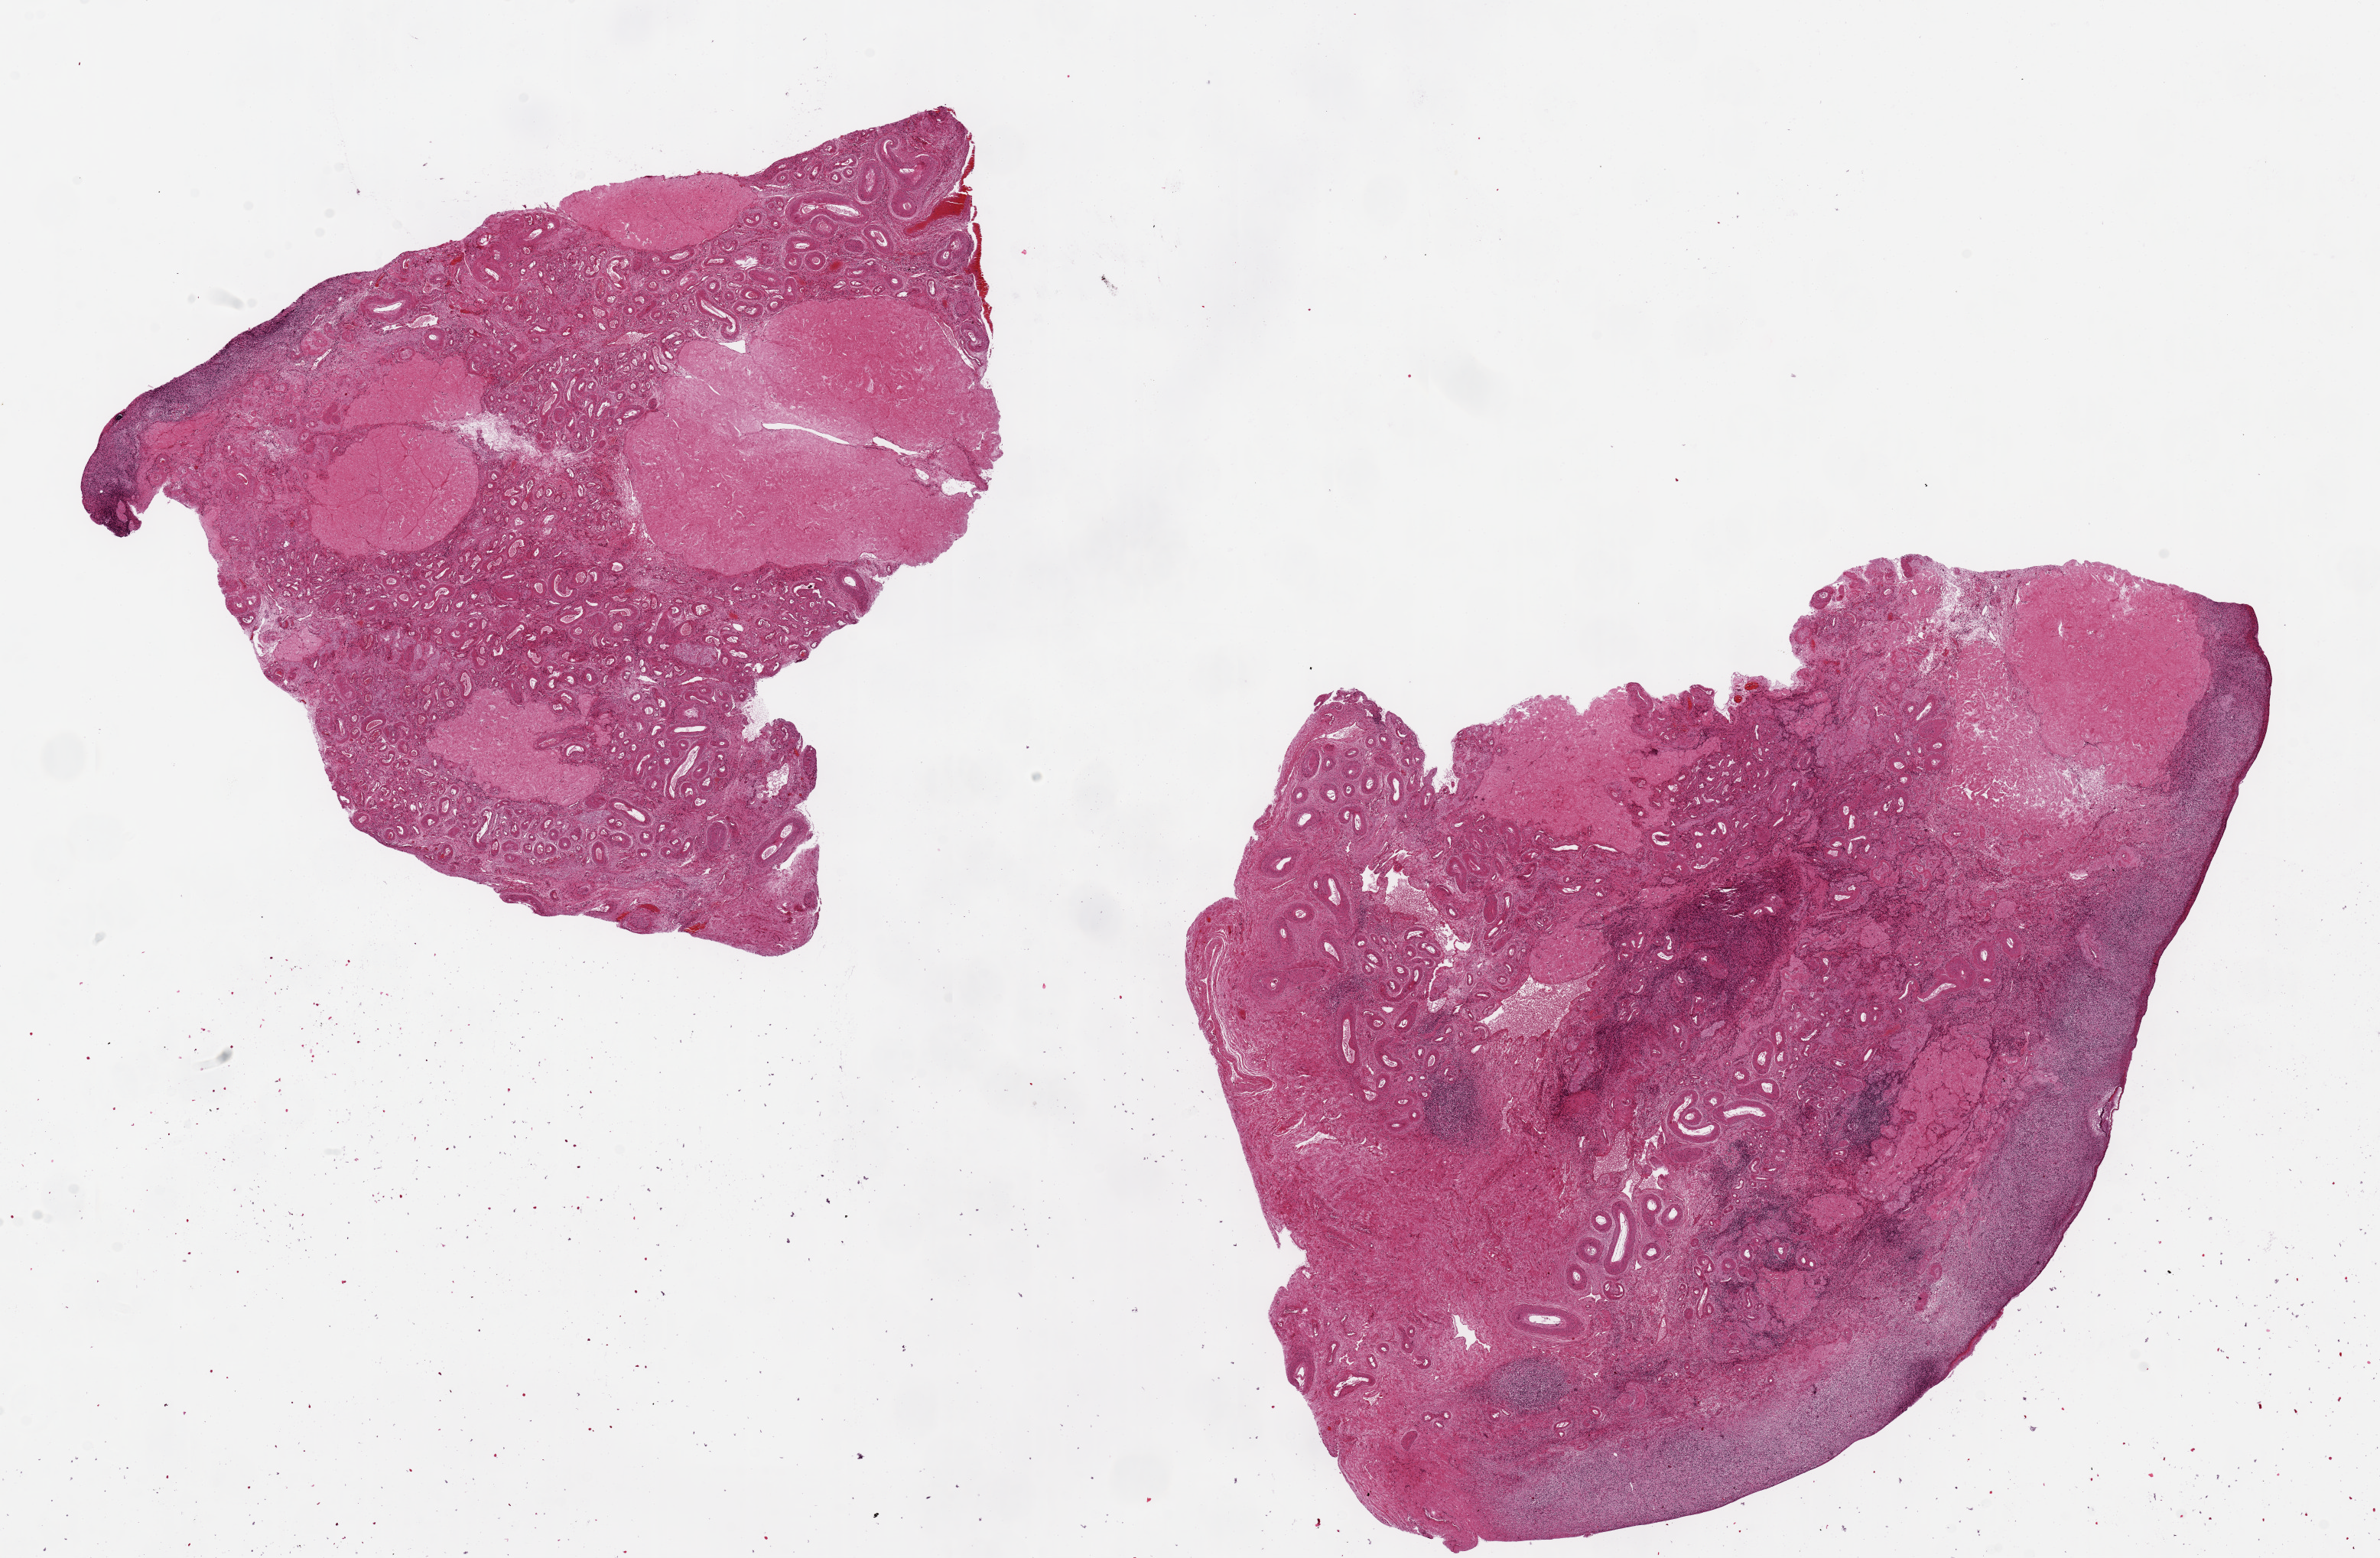
Hematoxylin and eosin (H&E) whole-slide image — shown as a low-resolution overview of the whole scanned area (about 24.6 x 16.1 mm, from a 20x scan). PAXgene-fixed paraffin-embedded (PFPE) section. Sampled site (target tissue): ovary. Donor tissue sample. Donor: female.
• pathologist's review note for this sample: 2 ~10x8mm aliquots. Post menopausal atrophic cortex, corpora albicantia noted